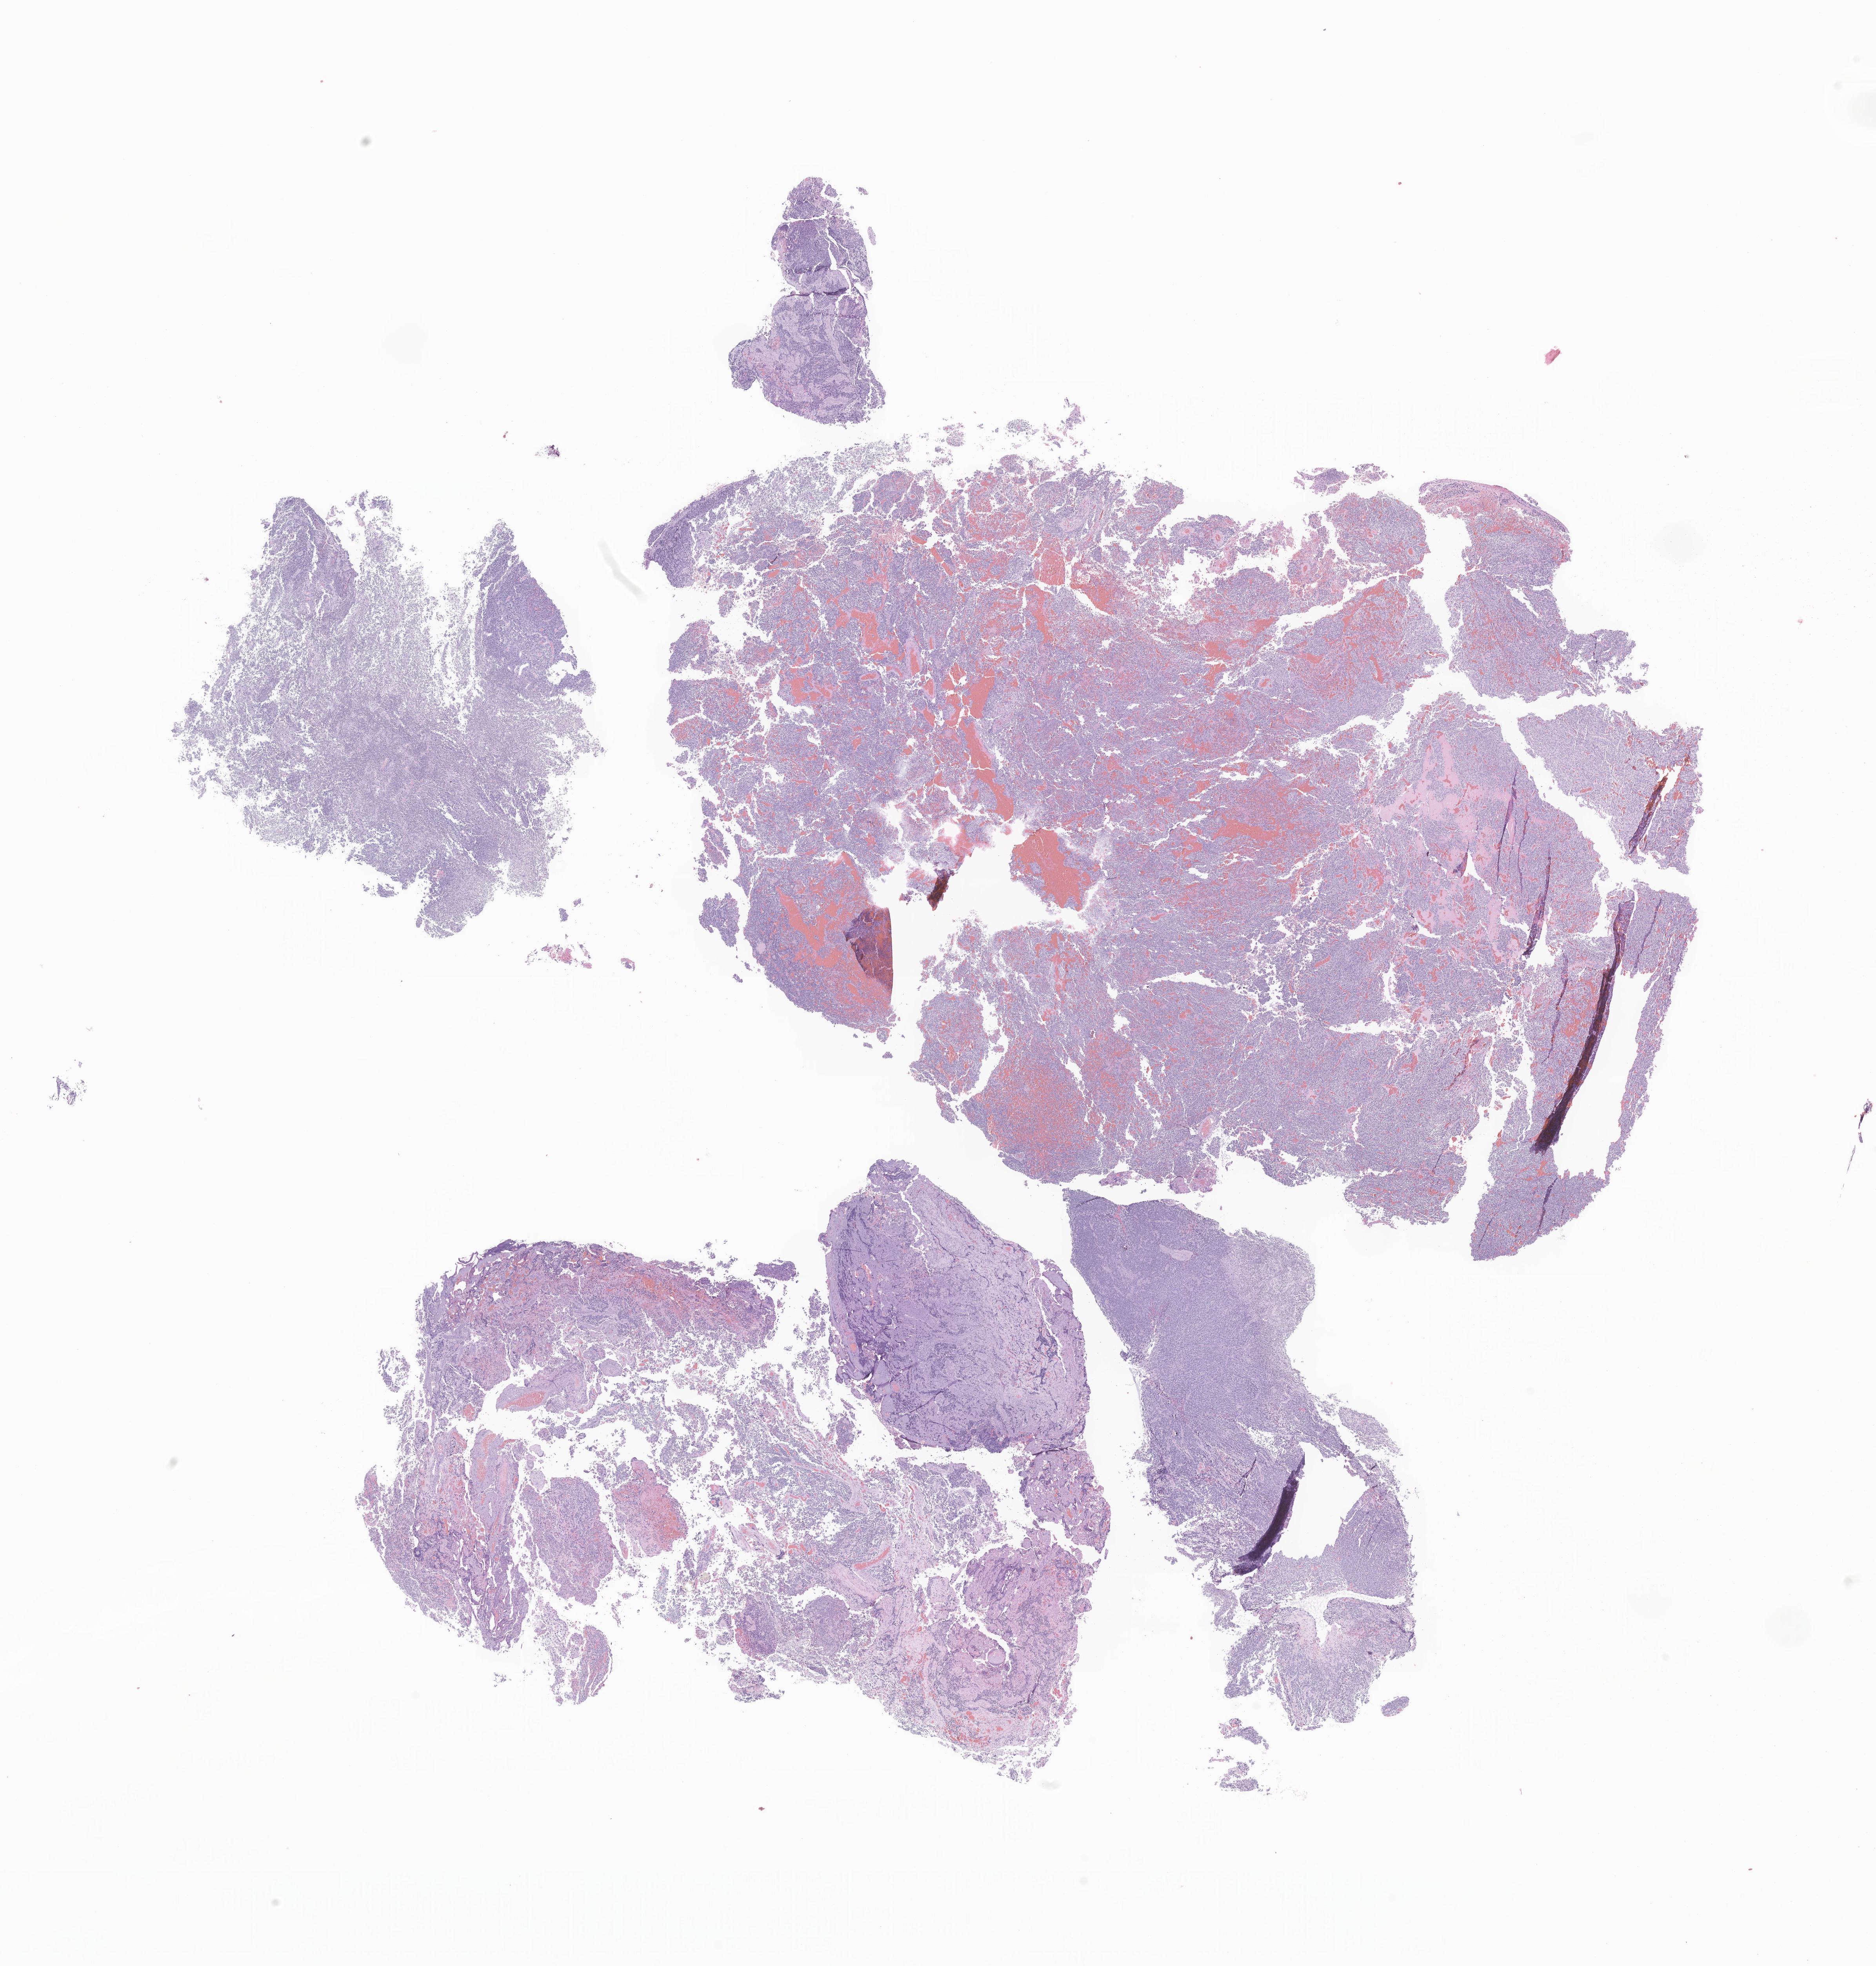
Digitized hematoxylin and eosin (H&E)-stained section of tumor tissue from the brain, low-resolution overview of the scanned area, about 20.2 x 21.1 mm; FFPE section. Patient: male, age 97 months.
Recorded diagnosis: Medulloblastoma, NOS.